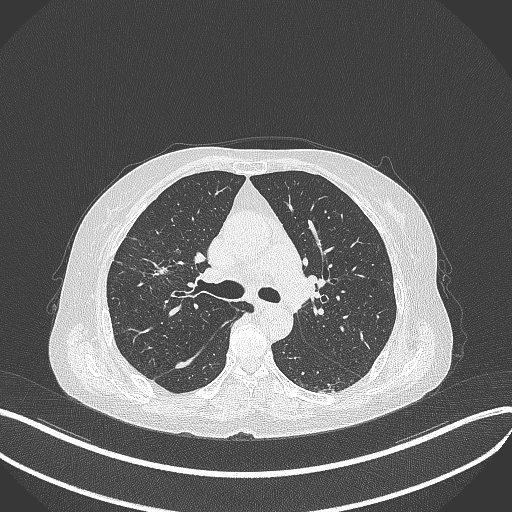
Chest CT, one axial slice; position 257 of 429 along the scan axis; reconstruction kernel B70f; 120 kVp; lung window (W 1500 / L -600 HU); 1 mm slice thickness; 512 × 512 image matrix, field of view 400 × 400 mm. Female patient, age 69 years. From the clinical record (not read from this slice): clinical TNM (as recorded): T1b N3 M0.
Structures marked on this image (bounding box drawn by a radiologist):
- lung tumour (recorded histology: small cell carcinoma): box from (x=136, y=256) to (x=176, y=286) px